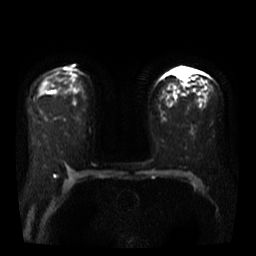
Breast MRI, one axial slice. Slice 23 of 40 in the series (ordered by position). Diffusion-weighted series; image 2 of 4 stored at this slice position (different b-values; order by instance number). 3 T. 5 mm slice thickness. 256 × 256 image matrix, field of view 360 × 360 mm. Female patient.
Annotated regions visible in this slice (outlined manually by an expert reader):
- tumour on diffusion-weighted imaging: bounding box (x1, y1, x2, y2) in pixels: (177, 69, 188, 77)